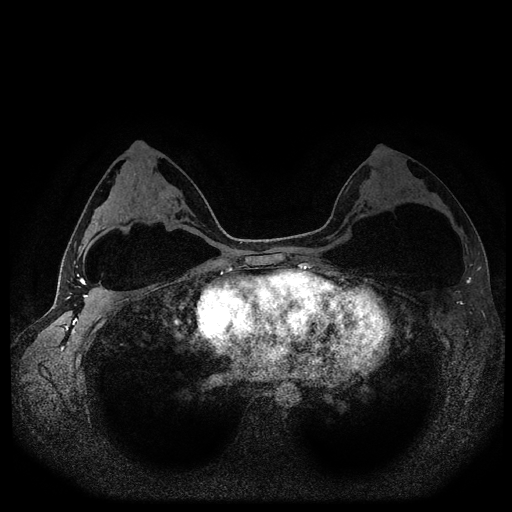
Breast MRI (dynamic contrast-enhanced, multi-phase), one axial slice; position 60 of 116 along the scan axis; dynamic contrast-enhanced series, time point 2 of 5 at this slice position (early post-contrast); 1.5 T; TE 2.6 ms, TR 5.4 ms; 2 mm slice thickness; 512 × 512 image matrix, field of view 340 × 340 mm. Female patient, age 33 years.
Outlined on this slice (semi-automatic segmentation, software-assisted and operator-edited):
- breast lesion (labelled benign in the annotation): bounding box [x1, y1, x2, y2] px = [159, 189, 181, 202]